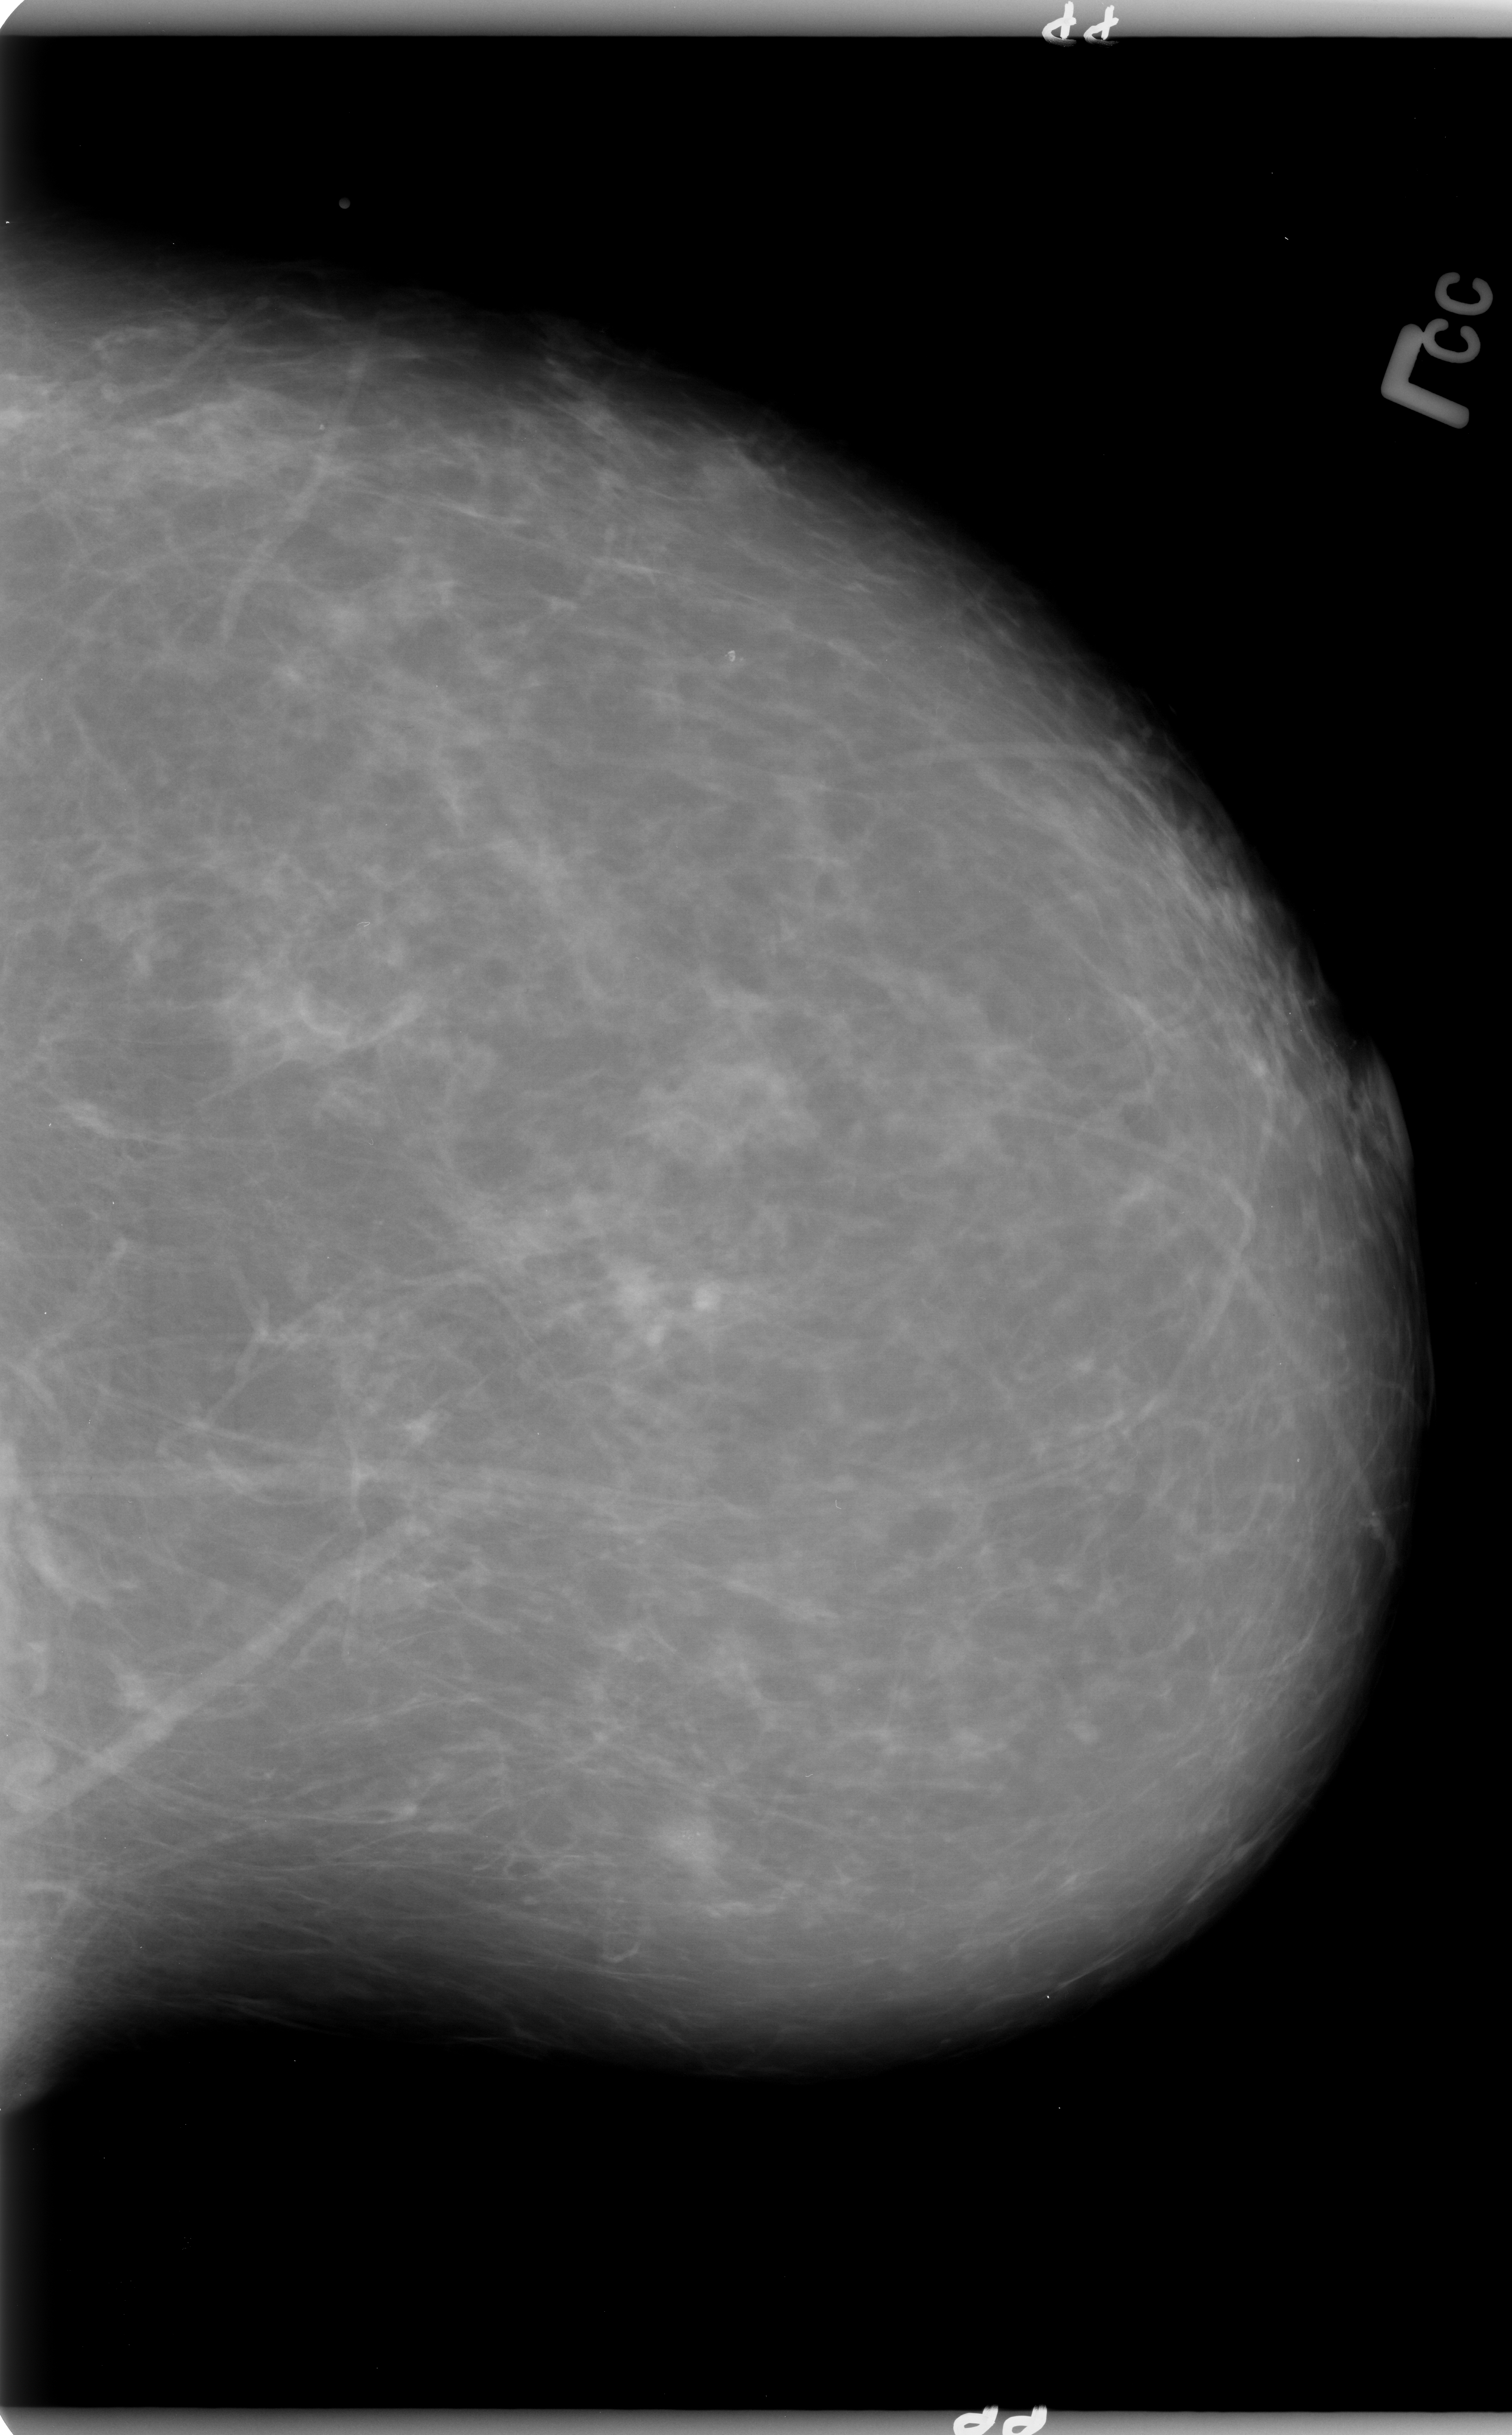
Mammogram (digitized film), left breast, CC view.
- Abnormality record for this image: calcifications, morphology pleomorphic, distribution clustered; BI-RADS assessment category 4; subtlety rating 3 on a 1 (subtle) to 5 (obvious) scale; pathology (as recorded): benign.